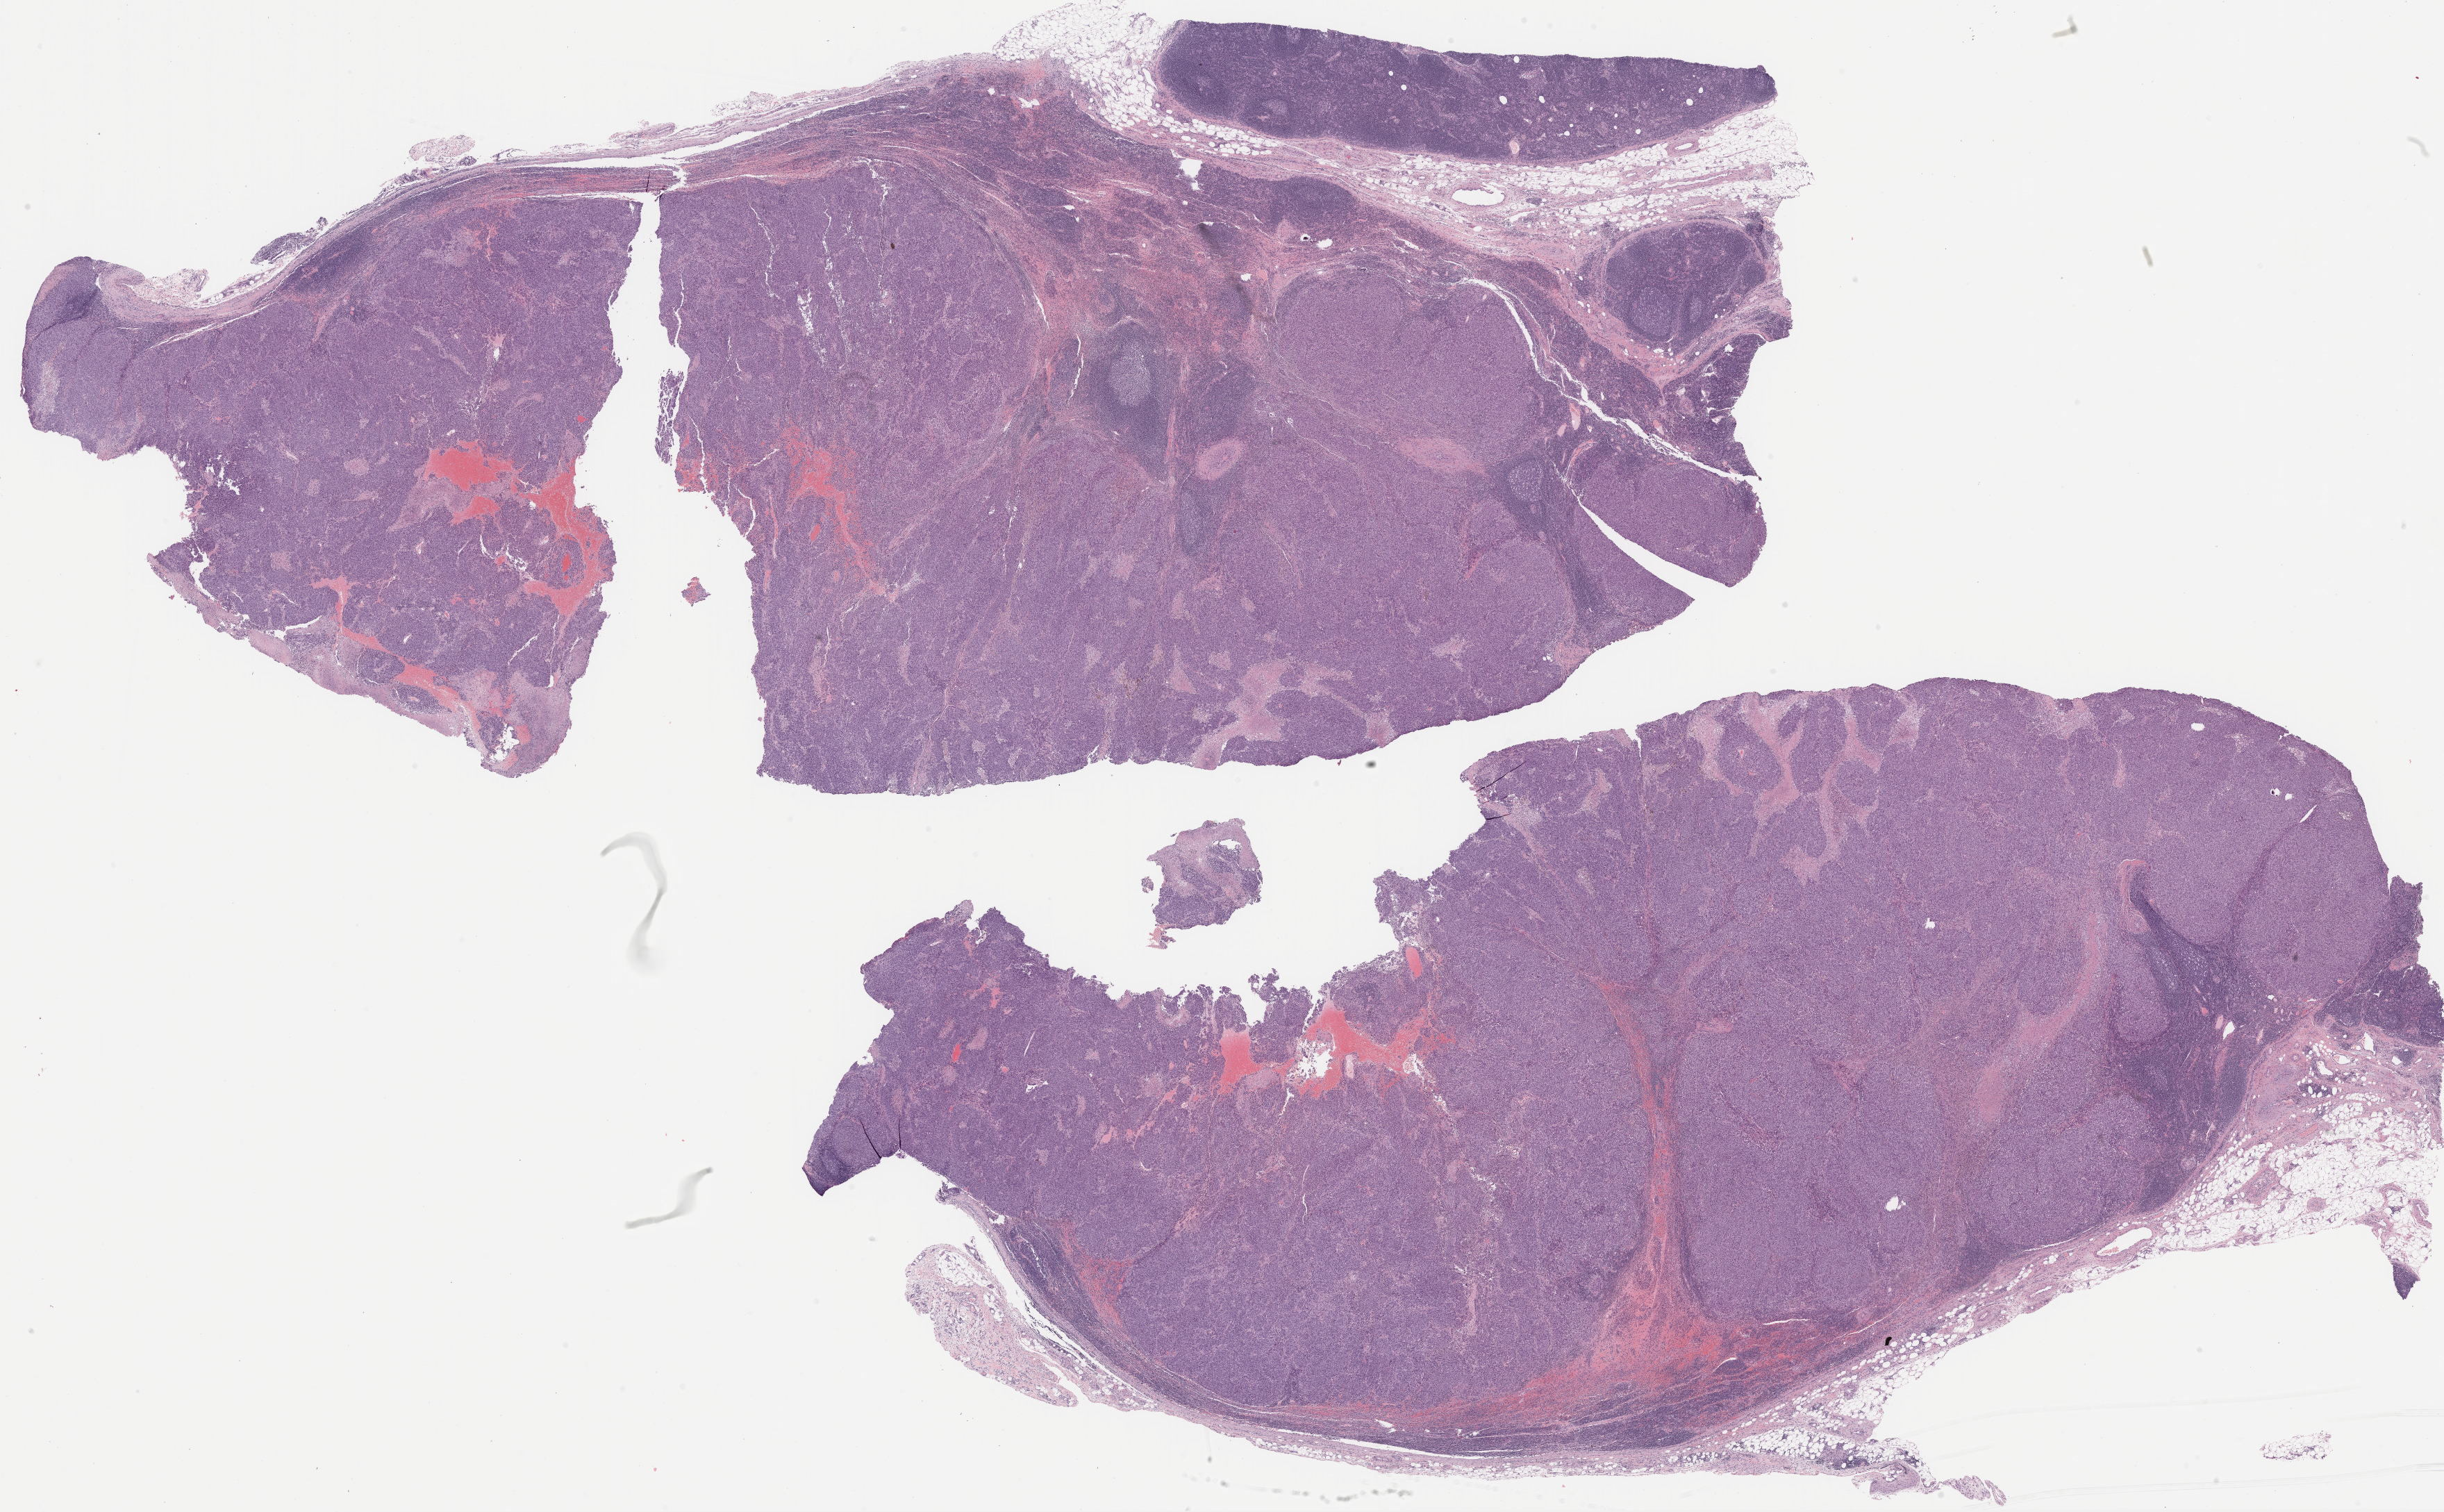
Whole-slide histology image, Hematoxylin and eosin (H&E) stained, shown as a low-resolution overview of the whole scanned area (about 28.4 x 17.6 mm, acquisition: 20x scan); formalin-fixed paraffin-embedded (FFPE) diagnostic section; metastatic tumour sample. Female patient; age at initial diagnosis 56 years.
This section: metastatic tumour tissue. Patient diagnosis: Malignant melanoma, NOS.